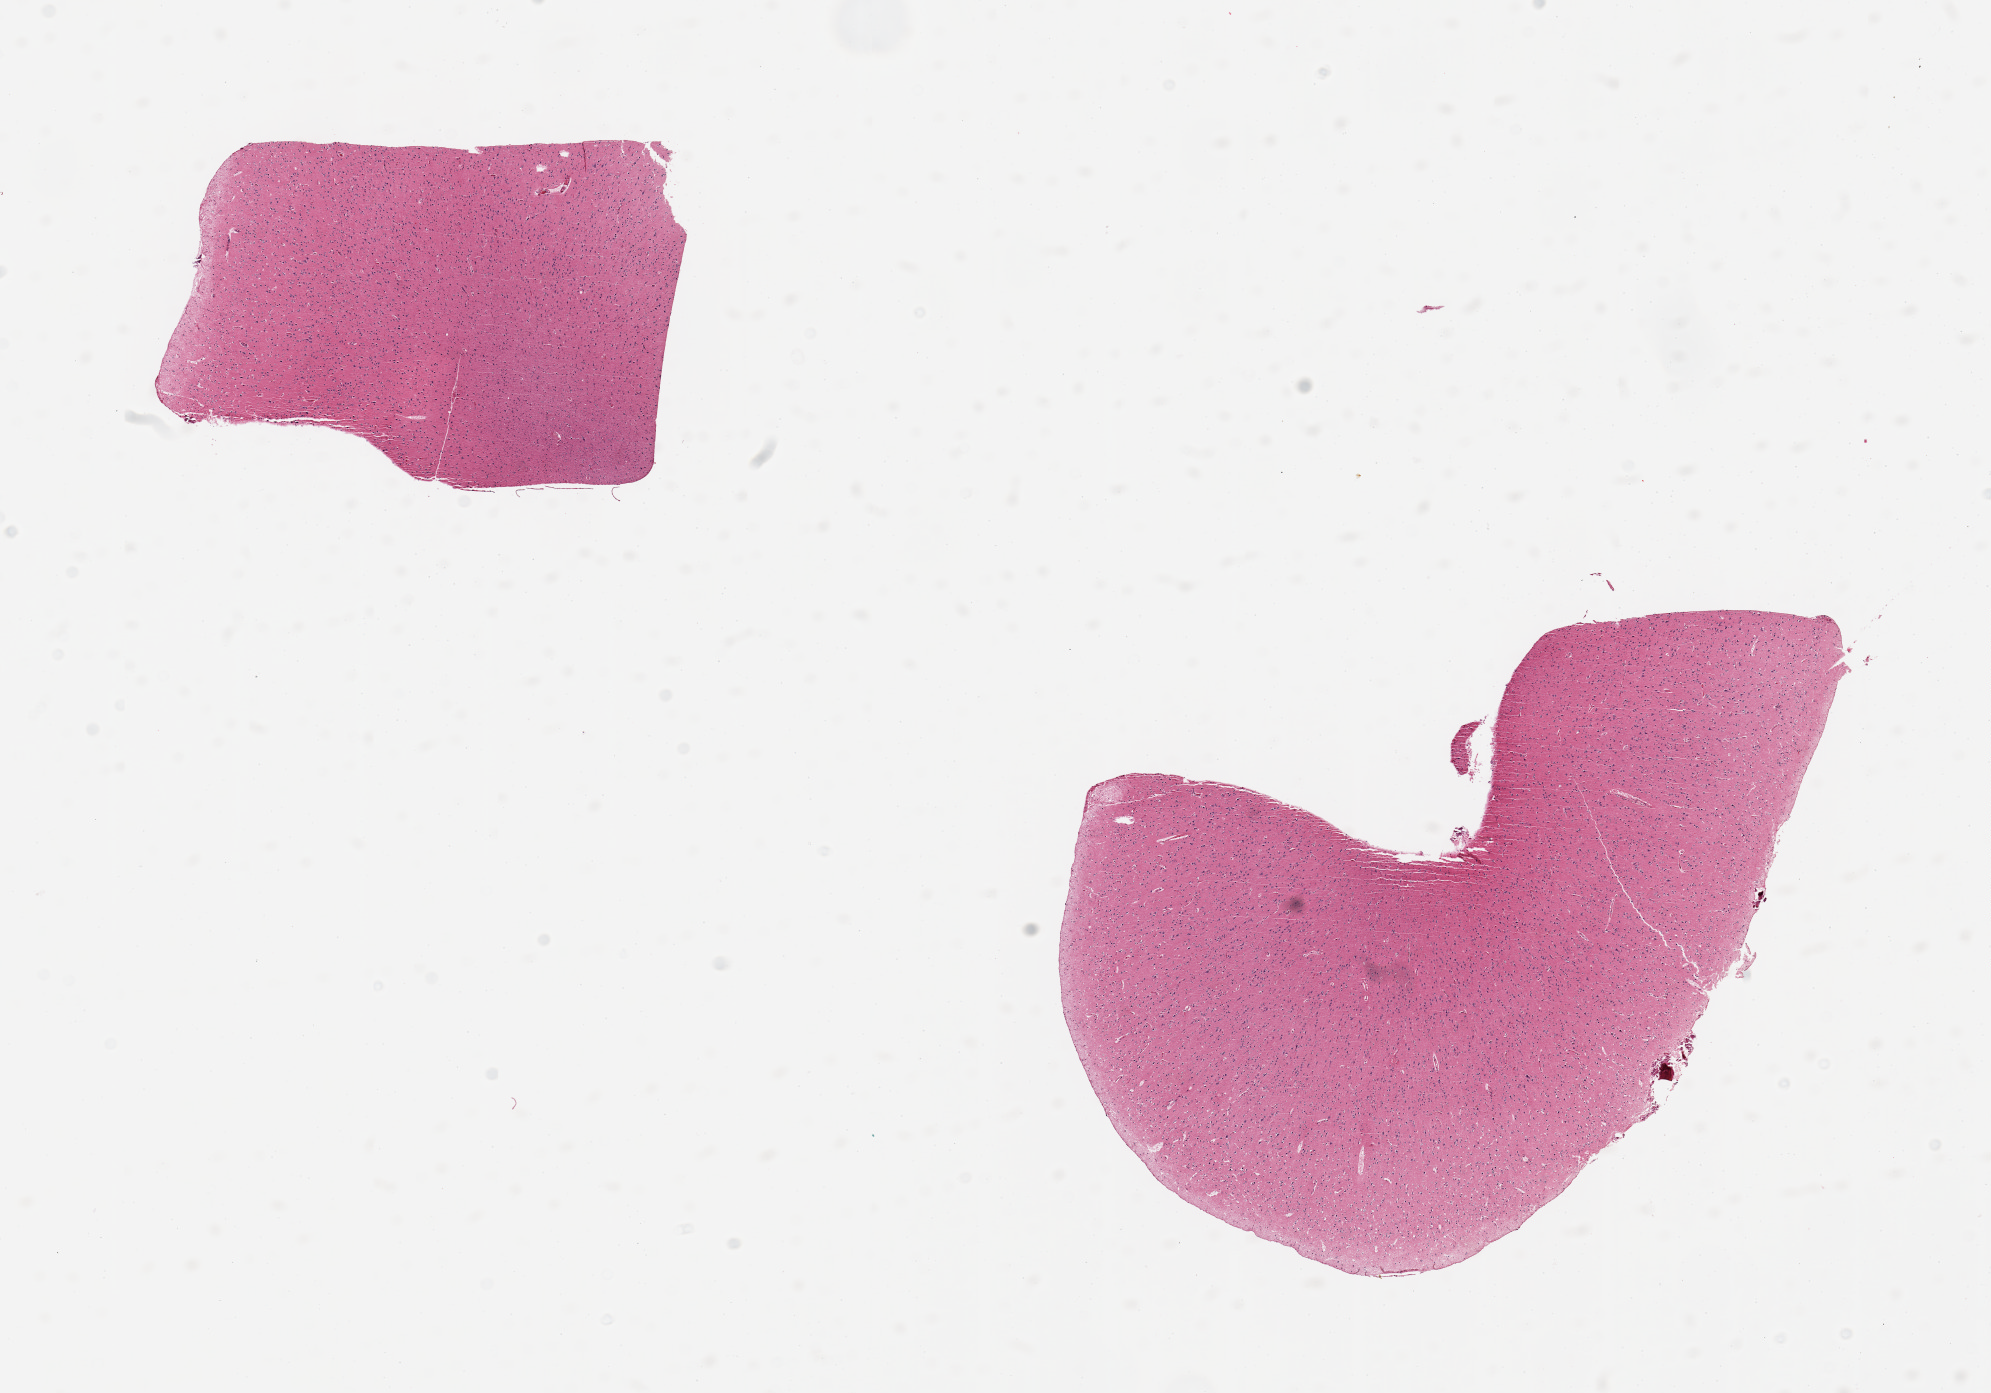
Digitized H&E-stained section, brightfield, low-resolution overview of the scanned area, about 15.8 x 11.0 mm (from a 20x scan). PAXgene-fixed paraffin-embedded (PFPE) section. Sampled site (target tissue): cerebral cortex. Donor tissue sample. Donor sex: male.
Review note (as recorded): 2 pieces; should have 4 pieces.